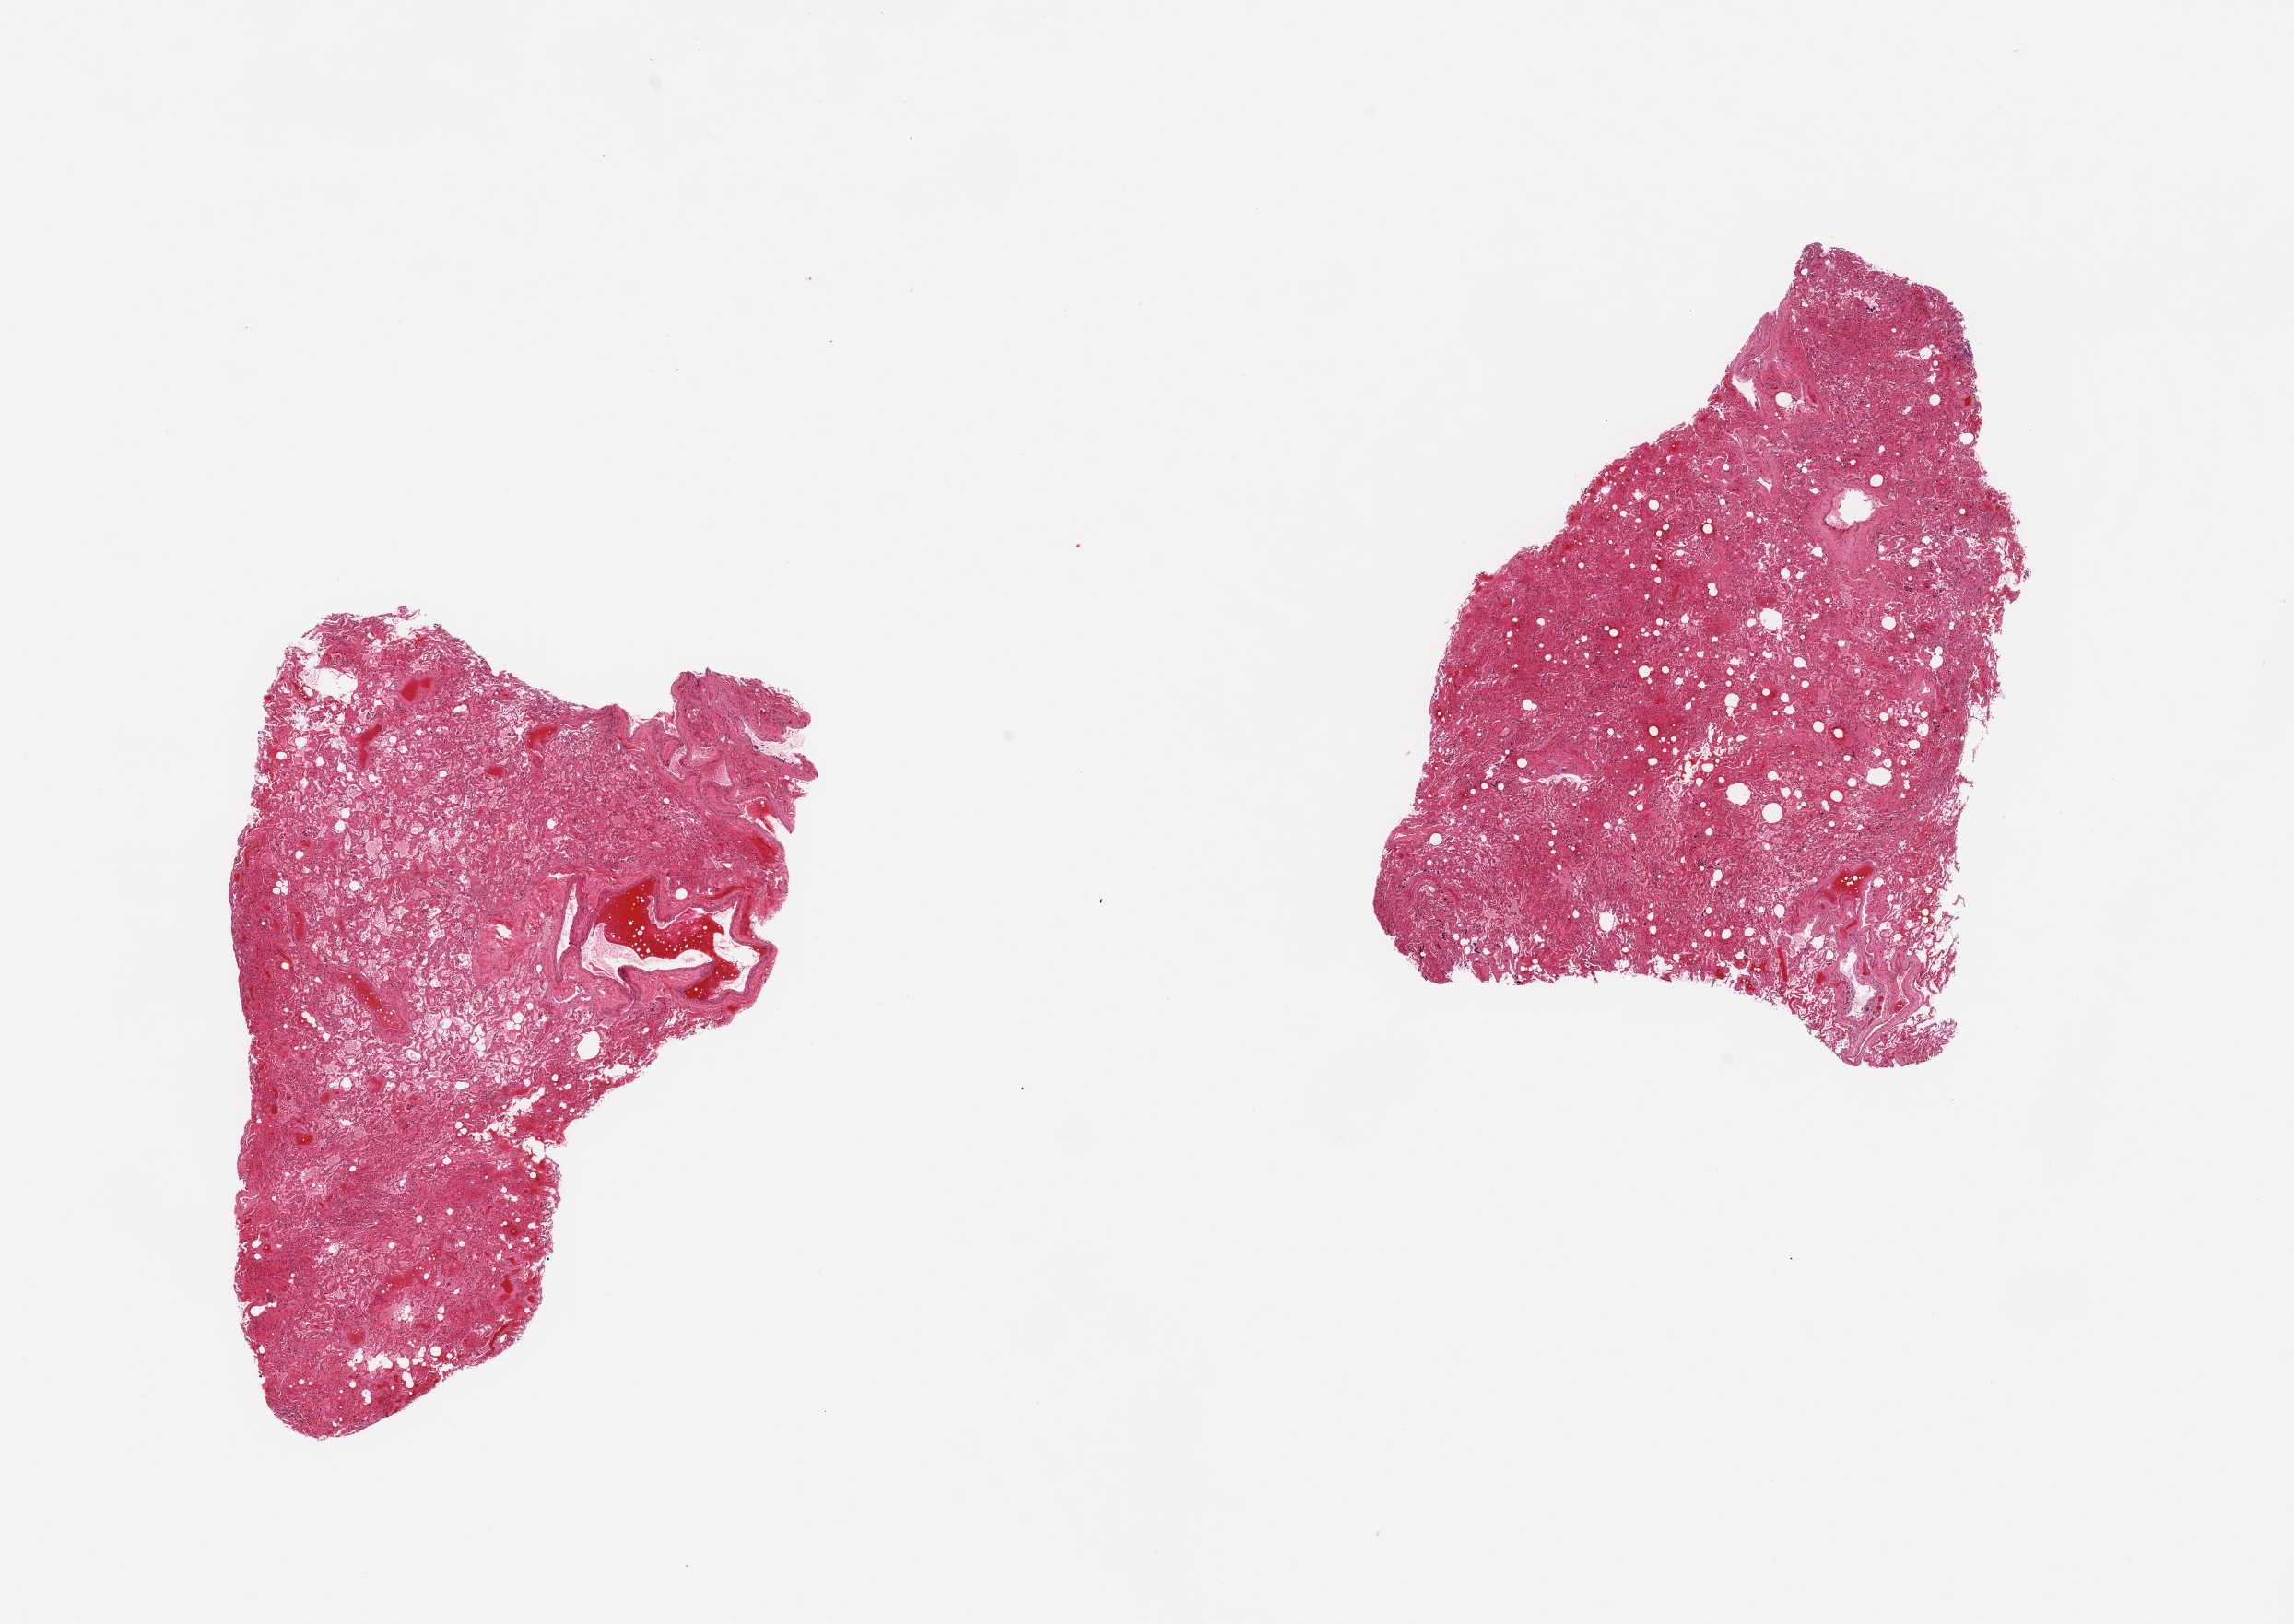
Hematoxylin and eosin (H&E) whole-slide image, shown as a low-resolution overview of the whole scanned area (about 19.7 x 13.9 mm, slide scanned at 20x), PAXgene-fixed paraffin-embedded (PFPE) section, sampled site (target tissue): lung, tissue donor sample.
* pathologist's review note for this sample: 2 pieces; moderate vascular congestion, alveolar hemorrhage and edema